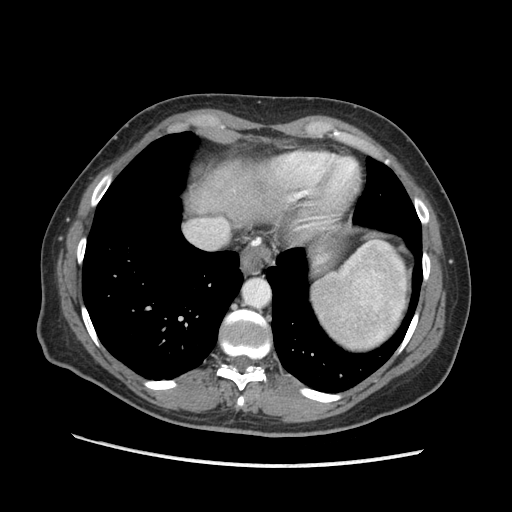
Contrast-enhanced abdominal CT (liver protocol), one axial slice. Slice 156 of 170 in the series (ordered by position). Soft-tissue window (W 400 / L 40 HU). 2.5 mm slice thickness. 512 × 512 image matrix. Case-level facts recorded for this patient, not image findings: diagnosis: hepatocellular carcinoma (patient treated with transarterial chemoembolisation; whether this scan precedes or follows treatment is not stated here); TNM stage (as recorded): Stage-II; Child-Pugh class: A; tumour differentiation: no biopsy; tumour nodularity: multinodular.
Structures marked on this image (semi-automatically segmented with operator editing):
- abdominal aorta: bounding box <244,280,269,306> (left, top, right, bottom; pixels)
- liver parenchyma outside the tumour (the mass and vessels are separate outlines, so this box may not span the whole liver): <206,164,238,186>